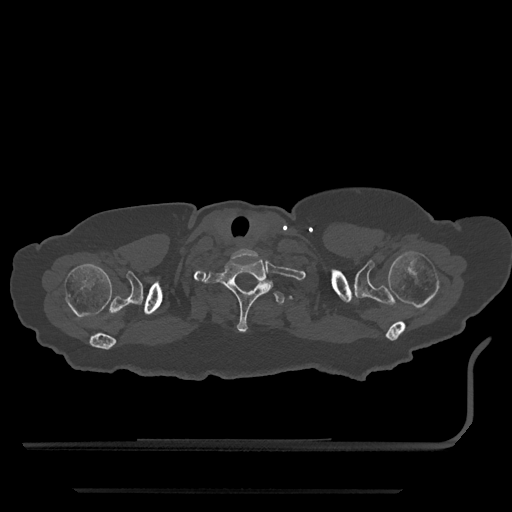
CT including the spine, one axial slice. Slice 708 of 797 in the series (ordered by position). 120 kVp. Bone window (W 1800 / L 400 HU). 0.5 mm slice thickness. 512 × 512 image matrix, field of view 440 × 440 mm. Female patient, age 51 years. Case-level facts recorded for this patient, not image findings: primary cancer: neuro.
Annotated regions visible in this slice (semi-automatically segmented with operator editing):
- T1 vertebra: bounding box [x1, y1, x2, y2] px = [205, 259, 273, 333]
- T2 vertebra: [256, 281, 285, 305]